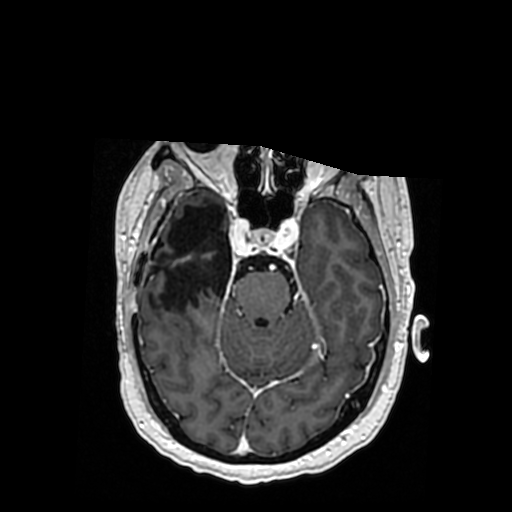
Brain MRI from a brain-tumour surgery series, one axial slice. Slice 231 of 364 in the series (ordered by position). T1-weighted post-contrast. 0.5 mm slice thickness. 512 × 512 image matrix, field of view 260 × 260 mm. From the clinical record (not read from this slice): histopathology: Oligodendroglioma; WHO grade: 3.
Structures marked on this image (expert manual segmentation):
- previous resection cavity: box from (x=151, y=205) to (x=231, y=312) px